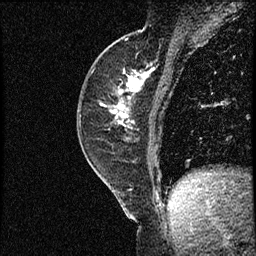
Breast MRI (dynamic contrast-enhanced), one sagittal slice. Slice 28 of 56 in the series (ordered by position). Dynamic contrast-enhanced study with each time point stored as its own series, time point 2 of 3 at this slice position (early post-contrast, ordered by acquisition time). 1.5 T. TE 4.2 ms, TR 17.3 ms. 2 mm slice thickness. 256 × 256 image matrix, field of view 200 × 200 mm. Female patient. From the clinical record (not read from this slice): setting: breast cancer imaged before/during neoadjuvant chemotherapy; receptor status: HER2-positive.
Annotated regions visible in this slice (semi-automatic segmentation, software-assisted and operator-edited):
- analysis volume of interest (the breast-tissue region the enhancement analysis was run in; not a lesion): bounding box (x1, y1, x2, y2) in pixels: (77, 50, 156, 155)
- tumour enhancement mask (voxels above the 100 % enhancement threshold inside the analysis volume of interest): (101, 70, 153, 126)